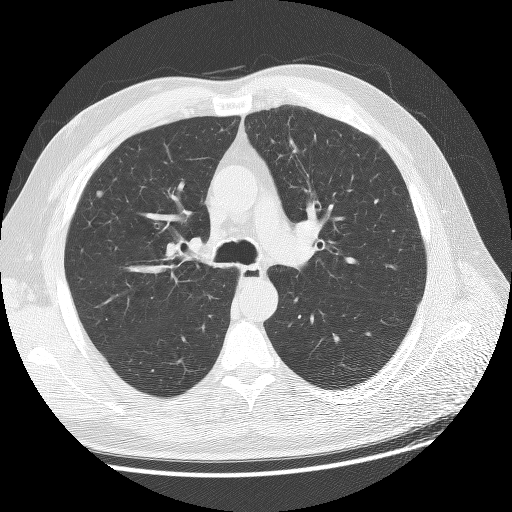
Low-dose screening chest CT, one axial slice. Position 95 of 137 along the scan axis. 120 kVp. Lung window (W 1500 / L -600 HU). 512 × 512 image matrix, field of view 380 × 380 mm.
Annotated regions visible in this slice (expert manual segmentation):
- lesion 1 (tumor): box from (x=97, y=191) to (x=102, y=197) px